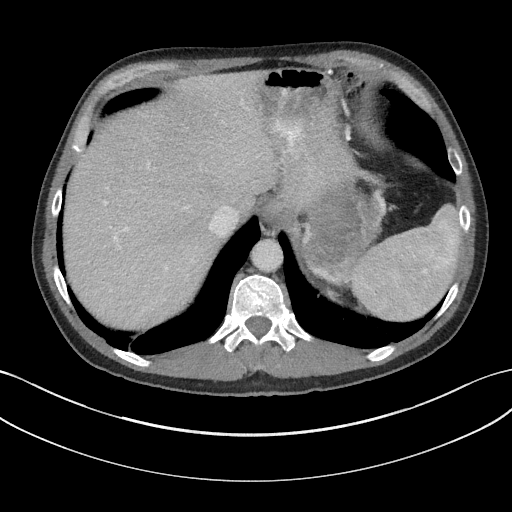
Contrast-enhanced abdominal CT, one axial slice. Slice 130 of 147 in the series (ordered by position). Intravenous contrast given. Soft-tissue window (W 400 / L 40 HU). 3 mm slice thickness. 512 × 512 image matrix. Patient: male, 58 years. From the clinical record (not read from this slice): diagnosis: adrenocortical carcinoma; tumour side: left adrenal; tumour size at pathology: 22 cm; Ki-67 index: 26 %; stage (as recorded): 2.
Structures marked on this image (semi-automatically segmented with operator editing):
- mass: box from (x=307, y=189) to (x=358, y=263) px